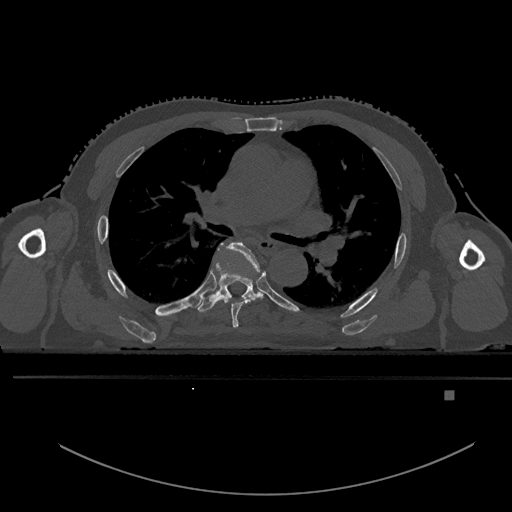
CT including the spine, one axial slice. Position 332 of 969 along the scan axis. Bone window (W 1800 / L 400 HU). 512 × 512 image matrix, field of view 456 × 456 mm. Male patient, age 82 years. From the clinical record (not read from this slice): primary cancer: prostate.
Structures marked on this image (semi-automatically segmented with operator editing):
- T5 vertebra: bounding box <221,242,262,328> (left, top, right, bottom; pixels)
- T6 vertebra: <192,243,262,313>